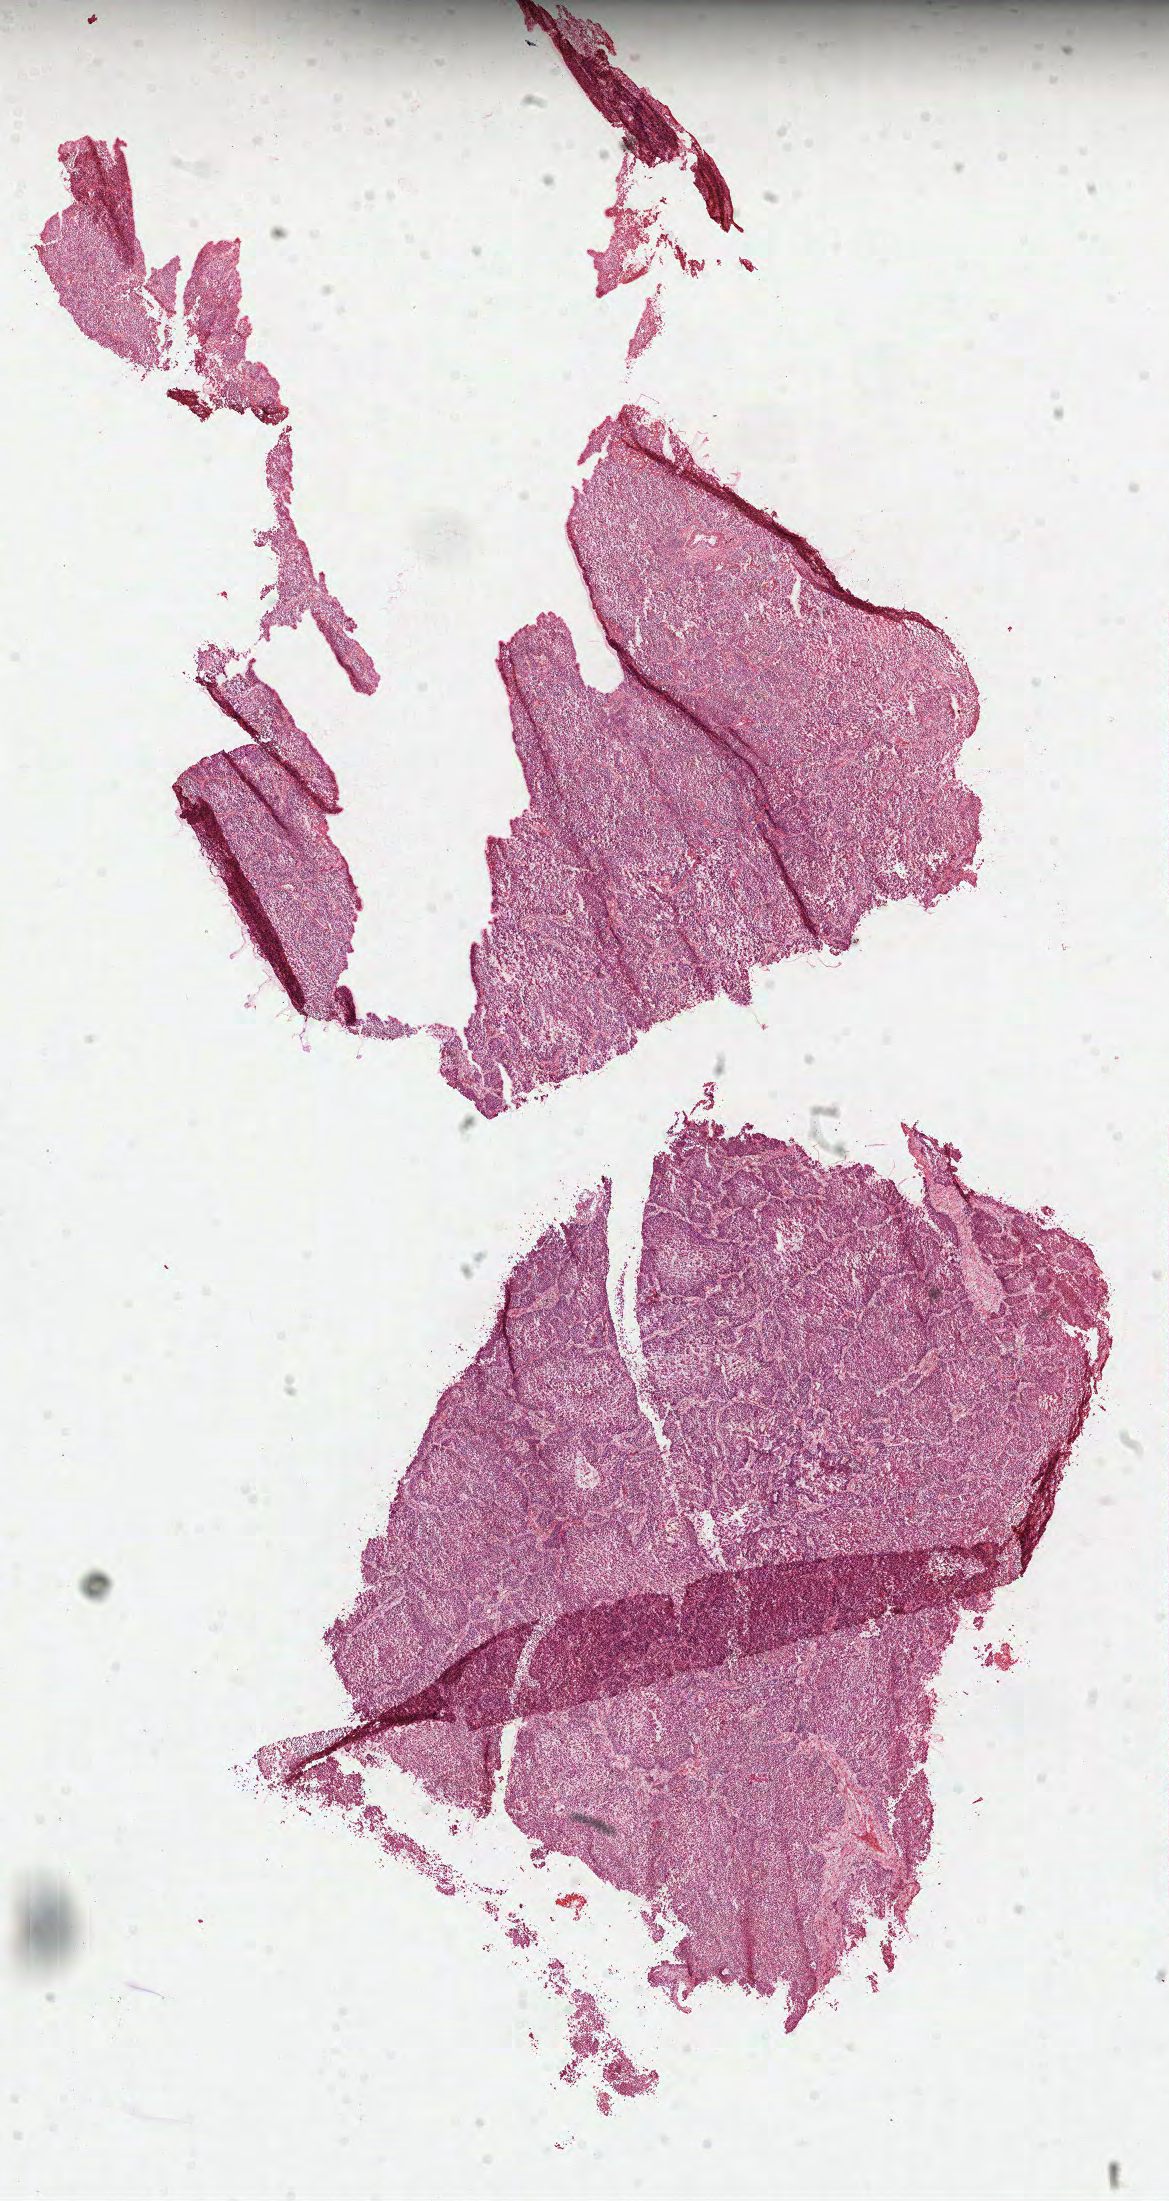
Digitized H&E tissue section (whole slide) — a low-resolution overview of the entire scanned area, about 9.4 x 17.7 mm (slide scanned at 40x), formalin-fixed paraffin-embedded (FFPE) diagnostic section, sample: primary tumour, lung. Male patient; age at initial diagnosis 77 years.
Diagnosis: Squamous cell carcinoma, NOS (lower lobe, lung).